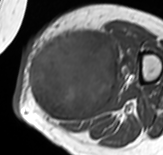
MRI of an extremity soft-tissue mass, one axial slice. Slice 31 of 65 in the series (ordered by position). MR volume resampled by the dataset authors to the PET/CT grid (not the native acquisition matrix). 3.27 mm slice thickness. 163 × 155 image matrix, field of view 159 × 151 mm. Female patient. Case-level facts recorded for this patient, not image findings: histological type: pleomorphic leiomyosarcoma; grade: high; site of the primary tumour: left thigh.
Structures marked on this image (expert contour drawn on MRI and transferred to this co-registered scan by the dataset authors):
- gross tumour volume including surrounding oedema: bounding box <28,29,118,125> (left, top, right, bottom; pixels)
- gross tumour volume (mass): <28,31,118,123>